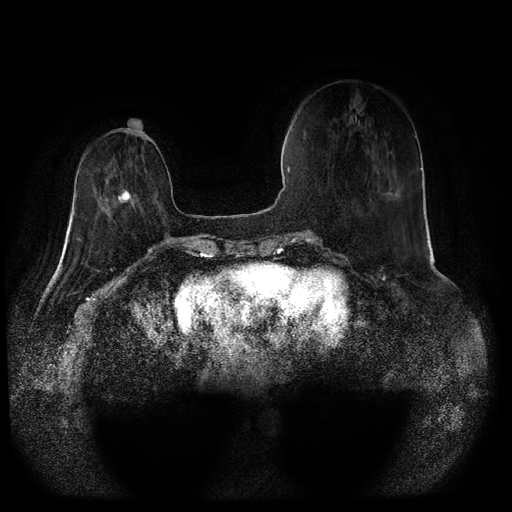
Breast MRI (dynamic contrast-enhanced, multi-phase), one axial slice; position 25 of 116 along the scan axis; dynamic contrast-enhanced series, time point 2 of 5 at this slice position (early post-contrast); 1.5 T; TE 2.6 ms, TR 5.3 ms; 2 mm slice thickness; 512 × 512 image matrix, field of view 360 × 360 mm. Female patient, age 71 years.
Outlined on this slice (semi-automatic segmentation, software-assisted and operator-edited):
- breast lesion (labelled 'tumour' in the annotation; benign lesions carry a separate 'benign' label): box from (x=116, y=189) to (x=134, y=204) px